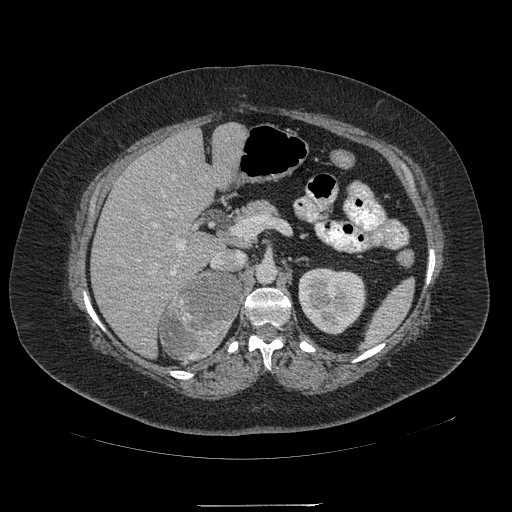
Contrast-enhanced abdominal CT, one axial slice; slice 125 of 217 in the series (ordered by position); reconstruction kernel STANDARD; intravenous contrast given; soft-tissue window (W 400 / L 40 HU); 1.25 mm slice thickness; 512 × 512 image matrix, field of view 453 × 453 mm. Patient: female, 55 years. From the clinical record (not read from this slice): diagnosis: adrenocortical carcinoma; tumour side: right adrenal; tumour size at pathology: 11 cm; Ki-67 index: 20 %; stage (as recorded): 2.
Annotated regions visible in this slice (semi-automatic segmentation, software-assisted and operator-edited):
- mass: bounding box (x1, y1, x2, y2) in pixels: (160, 273, 242, 358)